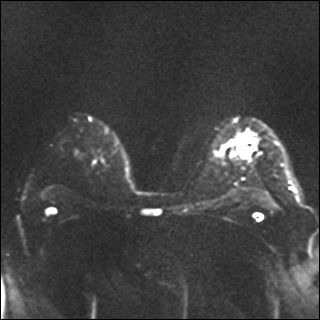
Breast MRI, one axial slice; position 22 of 35 along the scan axis; diffusion-weighted series; image 2 of 4 stored at this slice position (different b-values; order by instance number); 1.5 T; 4 mm slice thickness; 320 × 320 image matrix, field of view 320 × 320 mm. Female patient.
Outlined on this slice (outlined manually by an expert reader):
- tumour on diffusion-weighted imaging: box from (x=238, y=143) to (x=245, y=146) px